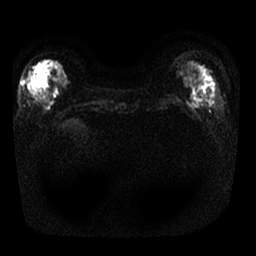
Breast MRI, one axial slice; position 7 of 25 along the scan axis; diffusion-weighted series; image 2 of 4 stored at this slice position (different b-values; order by instance number); 1.5 T; 256 × 256 image matrix, field of view 340 × 340 mm. Female patient.
Annotated regions visible in this slice (expert manual segmentation):
- tumour on diffusion-weighted imaging: bounding box <35,68,46,80> (left, top, right, bottom; pixels)